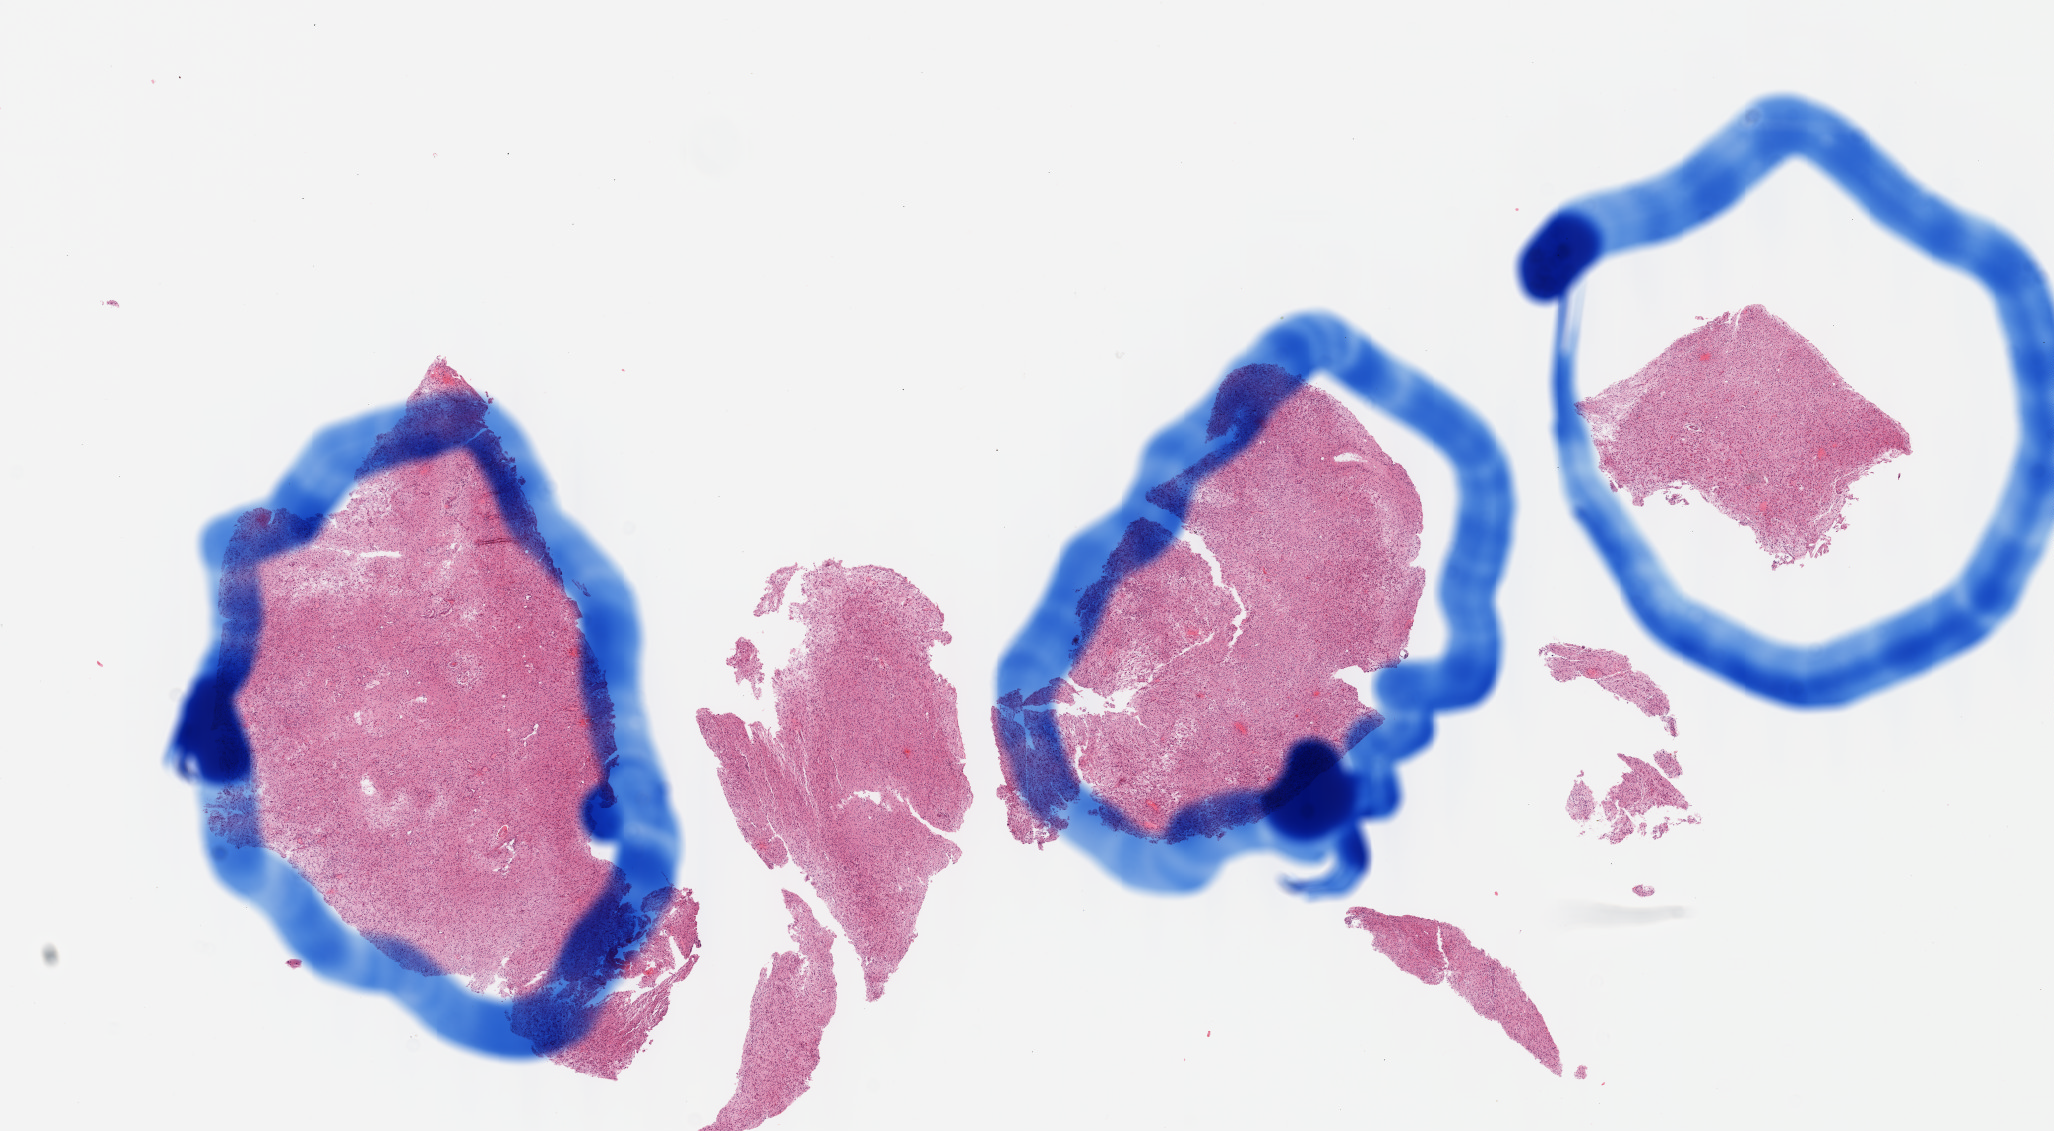
Whole-slide histology image, H&E — low-resolution overview of the scanned area, about 16.6 x 9.1 mm (acquisition: 40x scan), formalin-fixed paraffin-embedded (FFPE) diagnostic section, sample: primary tumour, brain. Female, age 71 years at initial diagnosis.
• pathologic diagnosis: Glioblastoma